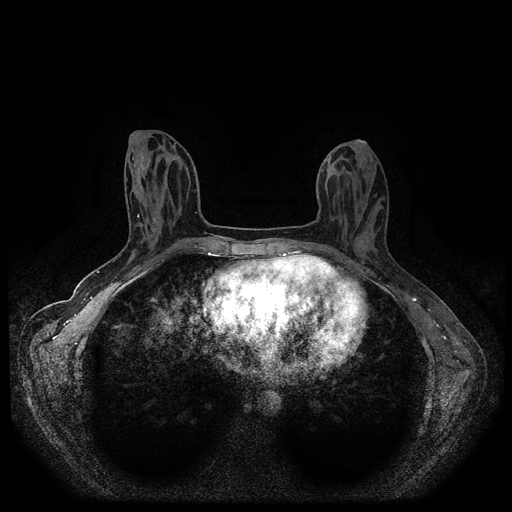
Breast MRI (dynamic contrast-enhanced, multi-phase), one axial slice. Slice 40 of 116 in the series (ordered by position). Dynamic contrast-enhanced series, time point 2 of 5 at this slice position (early post-contrast). 1.5 T. TE 2.6 ms, TR 5.4 ms. 2 mm slice thickness. 512 × 512 image matrix, field of view 340 × 340 mm. Female patient, age 30 years.
Structures marked on this image (semi-automatic segmentation, software-assisted and operator-edited):
- breast lesion (labelled benign in the annotation): bounding box <355,232,370,251> (left, top, right, bottom; pixels)